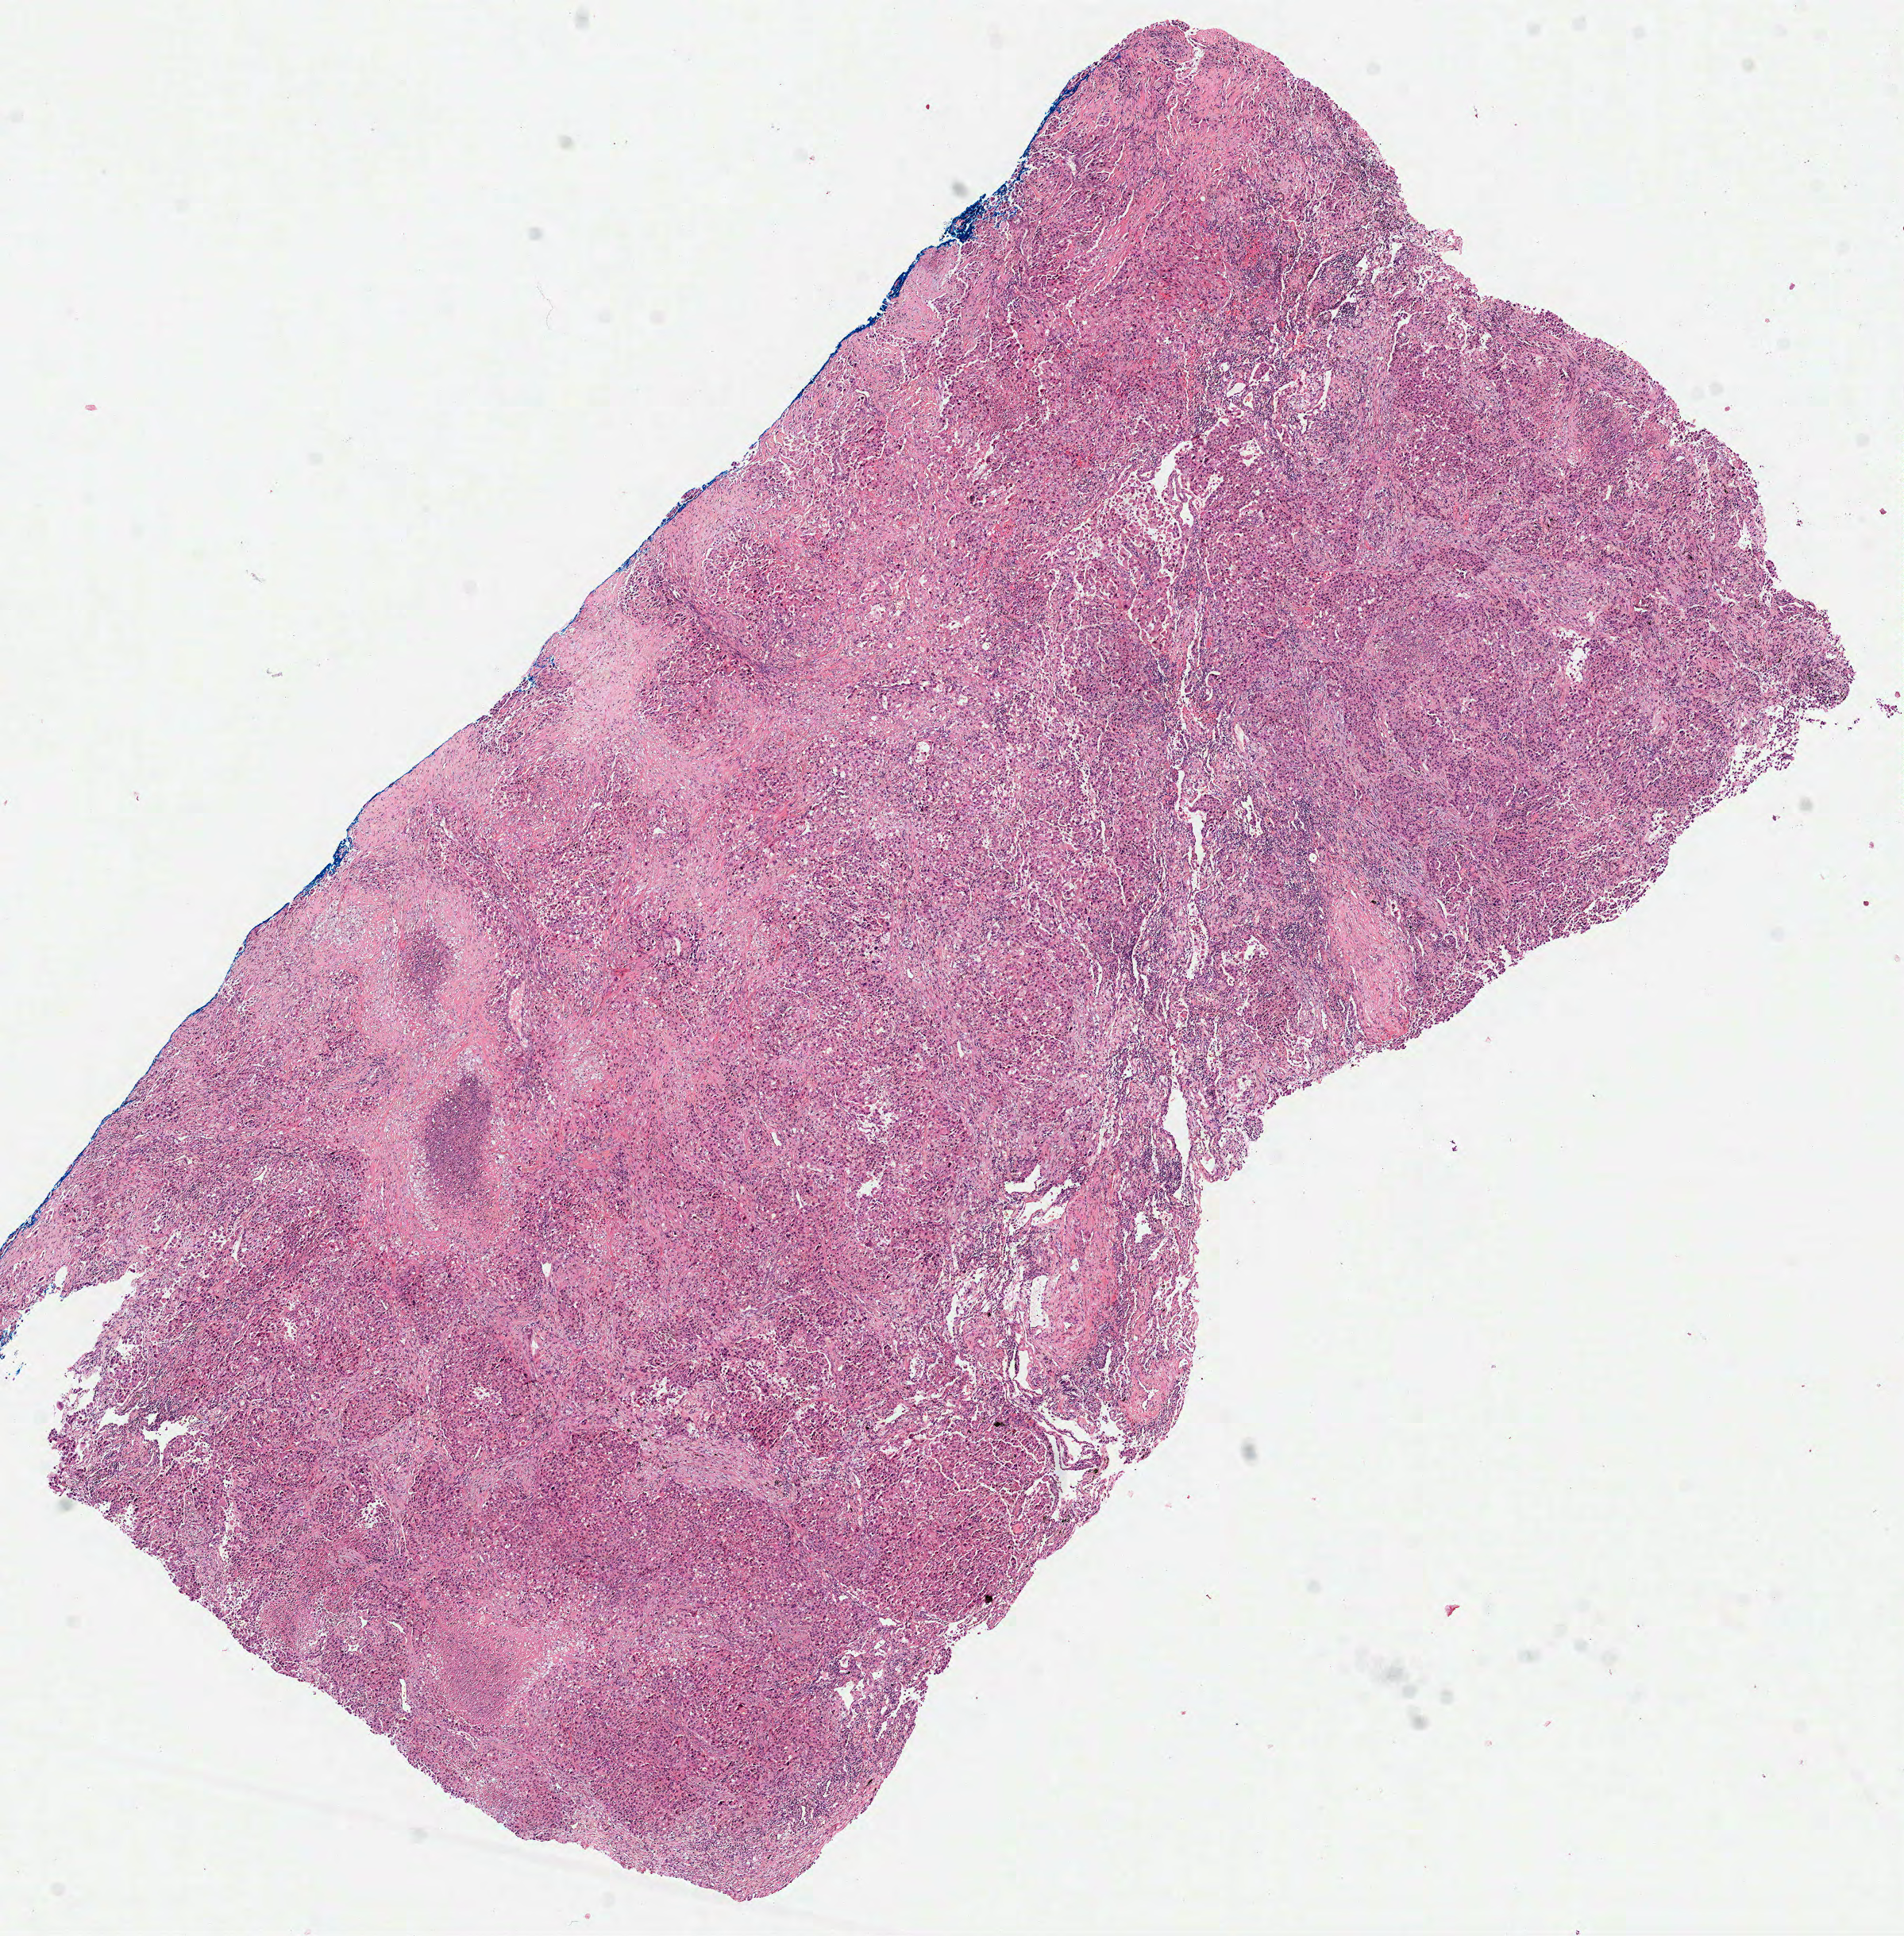
H&E-stained whole-slide image — whole scanned area (about 9.7 x 9.8 mm, from a 40x scan) shown as a low-resolution overview. FFPE section. Lung, primary tumour sample. Female, age 62 years at initial diagnosis.
Histologic diagnosis: Adenocarcinoma, NOS (upper lobe, lung). AJCC pathologic stage: IIB.